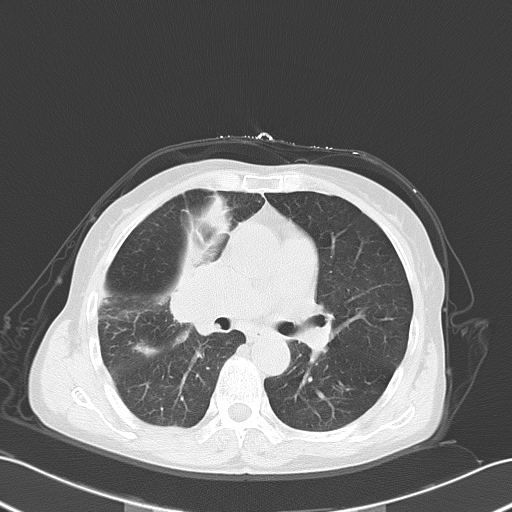
Chest CT, one axial slice. Reconstruction kernel B70f. 120 kVp. Lung window (W 1500 / L -600 HU). 5 mm slice thickness. 512 × 512 image matrix. Female patient, age 67 years. Case-level facts recorded for this patient, not image findings: clinical TNM (as recorded): T2a N3 M0; histopathological grade: G3.
Outlined on this slice (rectangle marked by the reading radiologist):
- lung tumour (recorded histology: small cell carcinoma): box from (x=169, y=266) to (x=233, y=332) px